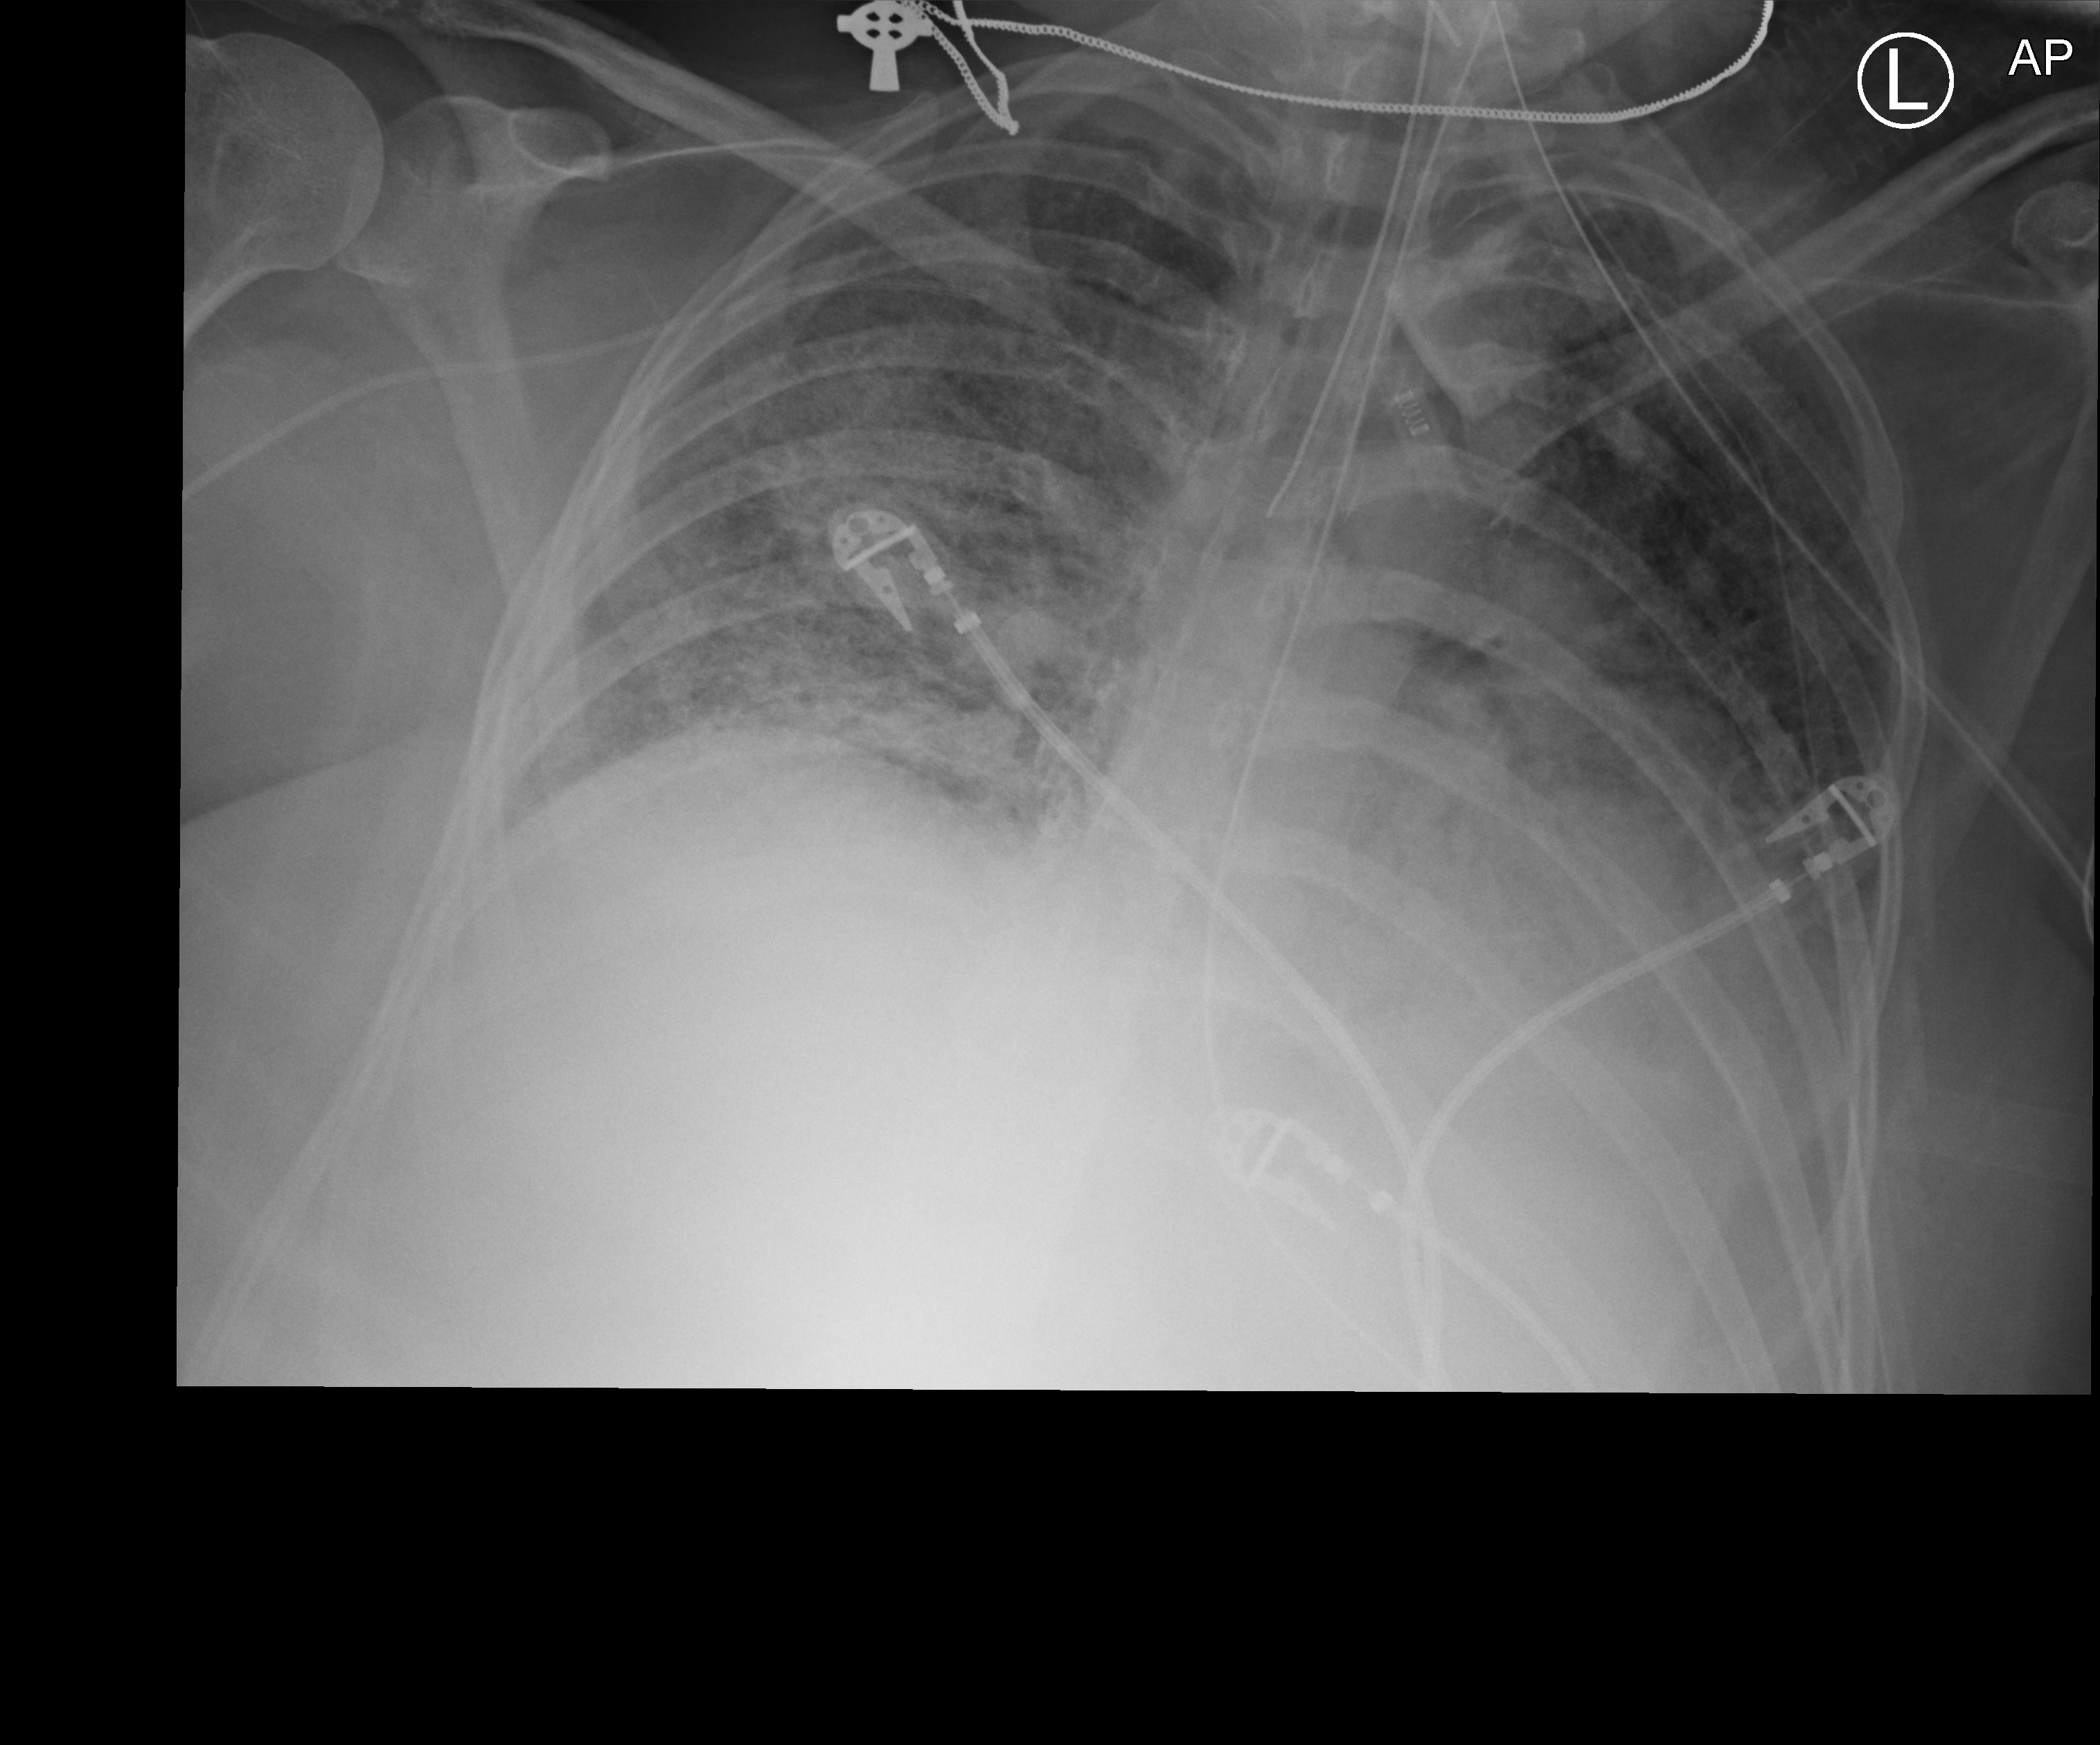
Bedside chest radiograph (computed radiography); anteroposterior (AP) projection. Patient hospitalised with COVID-19; female, aged 18–59 years.
Hospital-stay facts (about this admission, not read from this image; timing relative to this image not recorded): mechanically ventilated during this hospital stay: yes; admitted to intensive care during this hospital stay: yes.